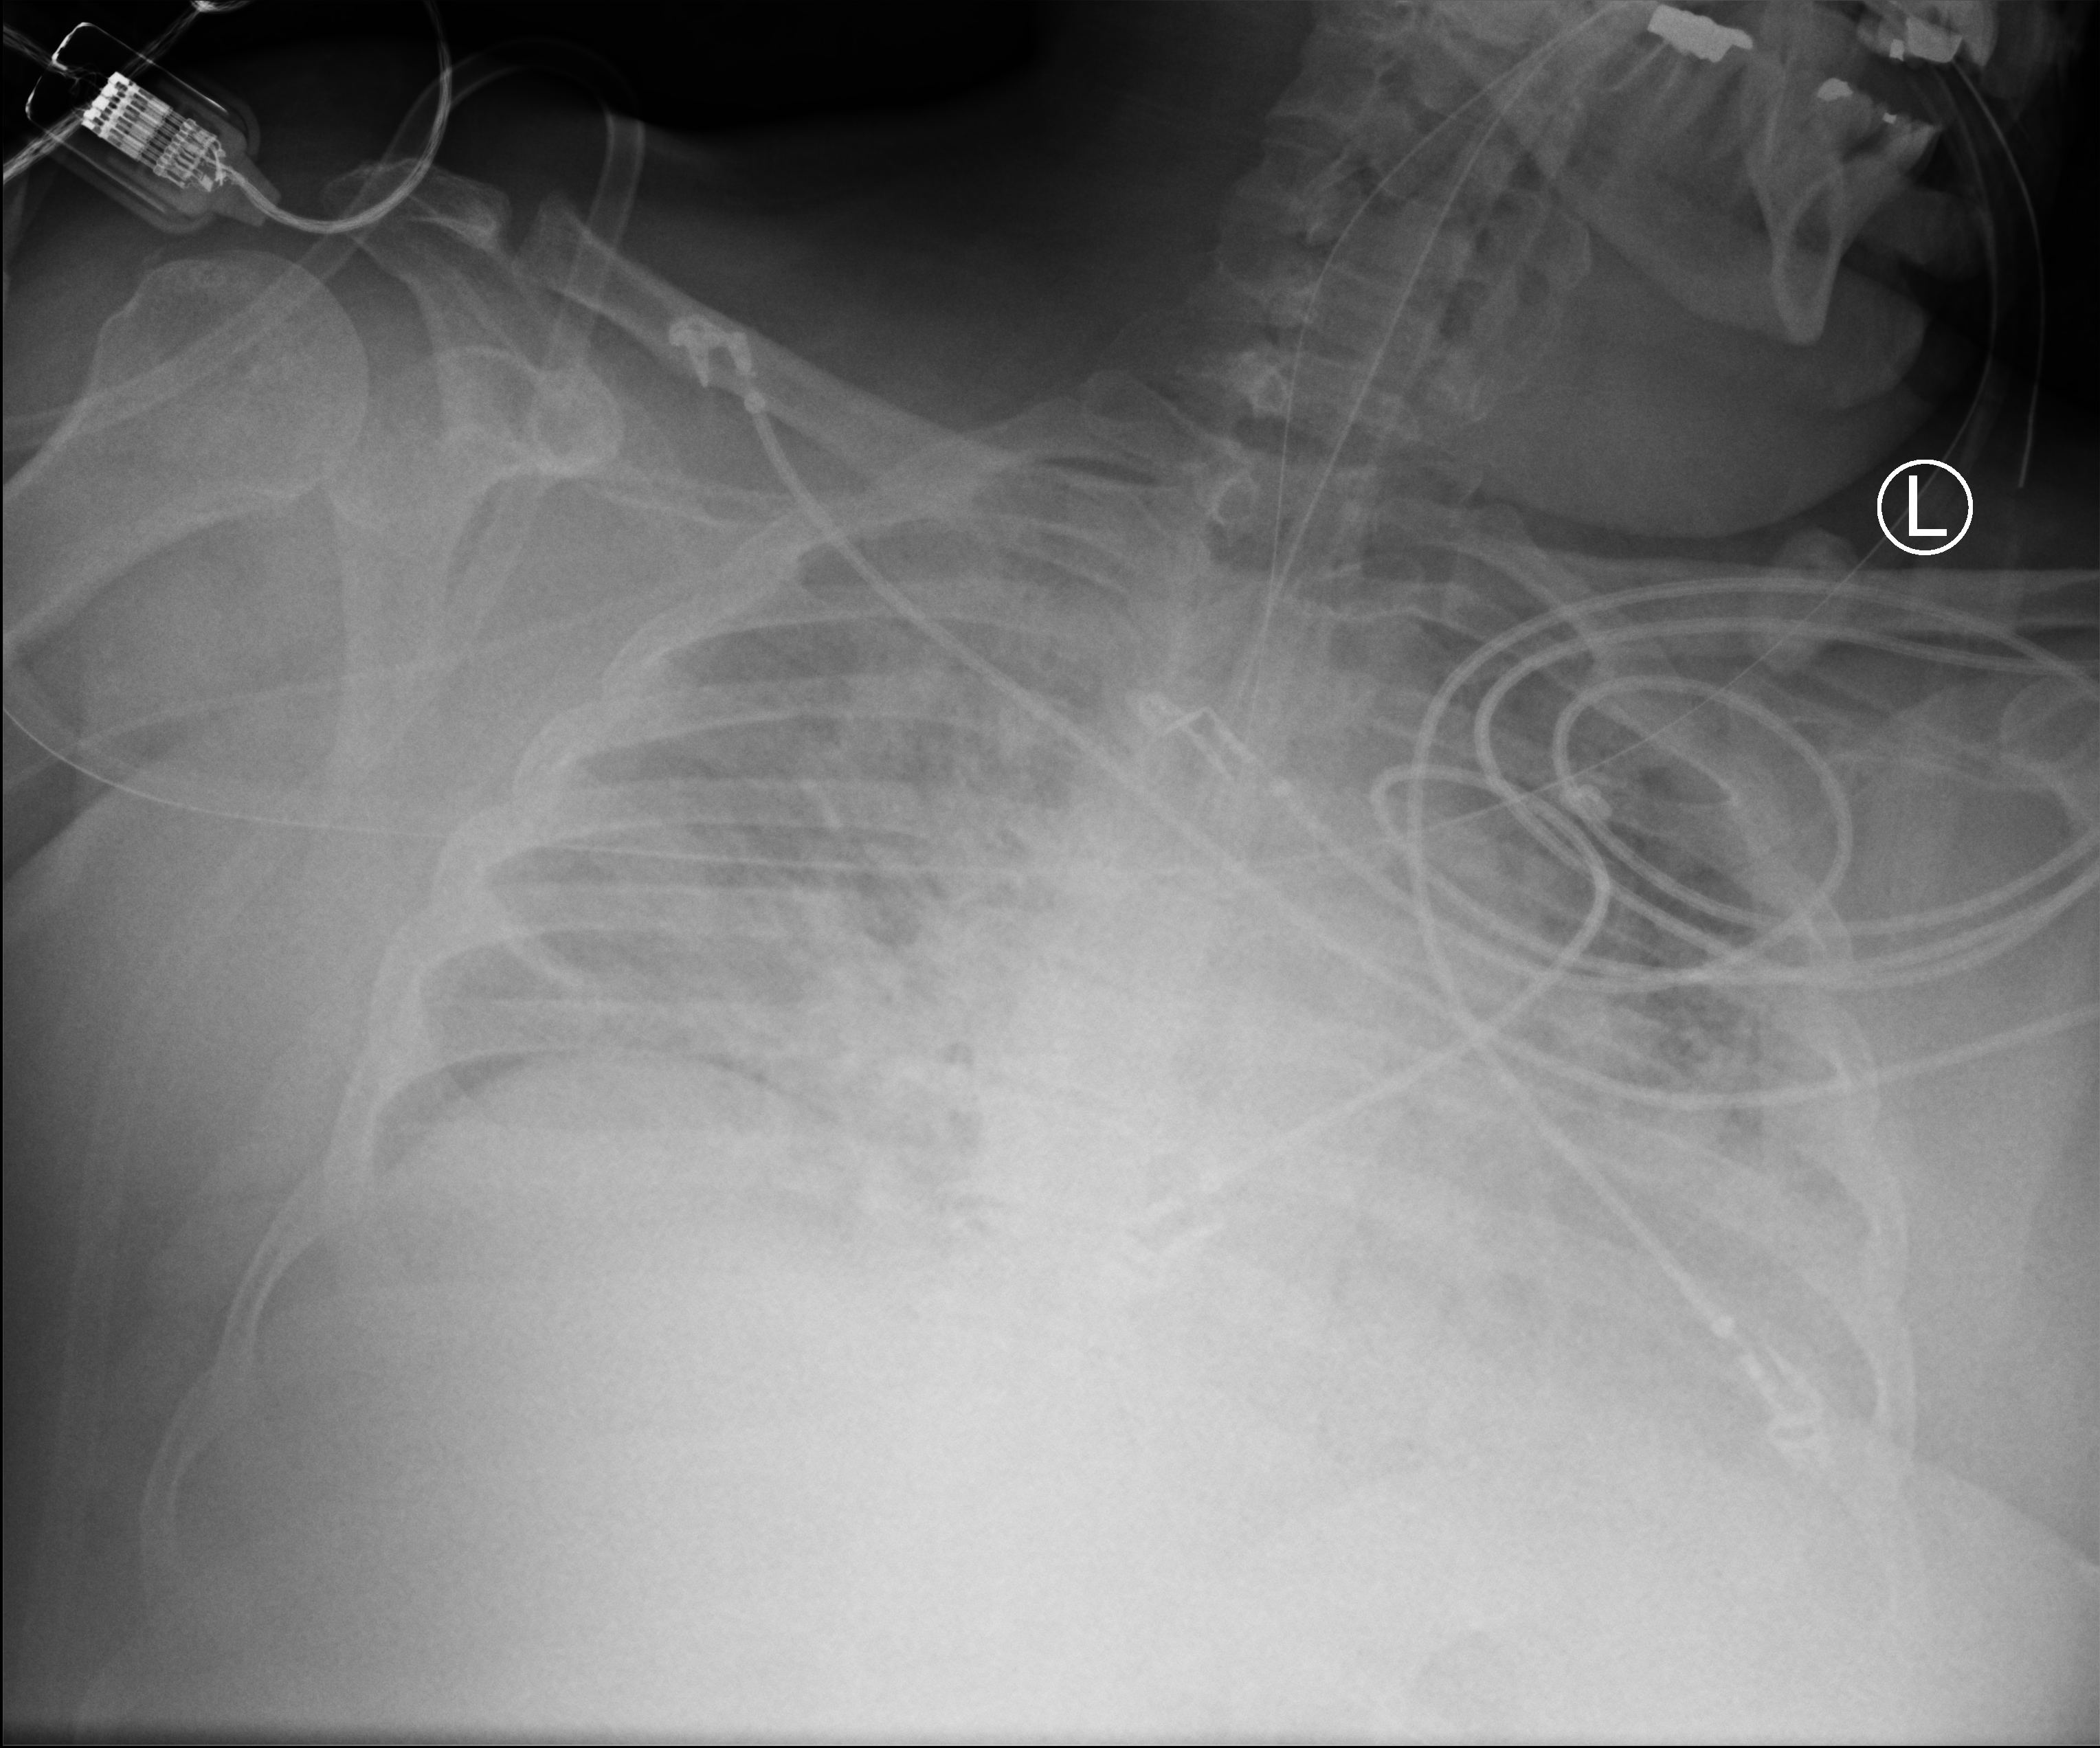
Chest X-ray (portable); anteroposterior (AP) projection. Patient hospitalised with COVID-19; male, aged 18–59 years.
Admission-level facts for this patient (not findings on this image; timing relative to this image not recorded): hypertension (admission record): no; length of hospital stay: 28 days; admitted to intensive care during this hospital stay: yes.